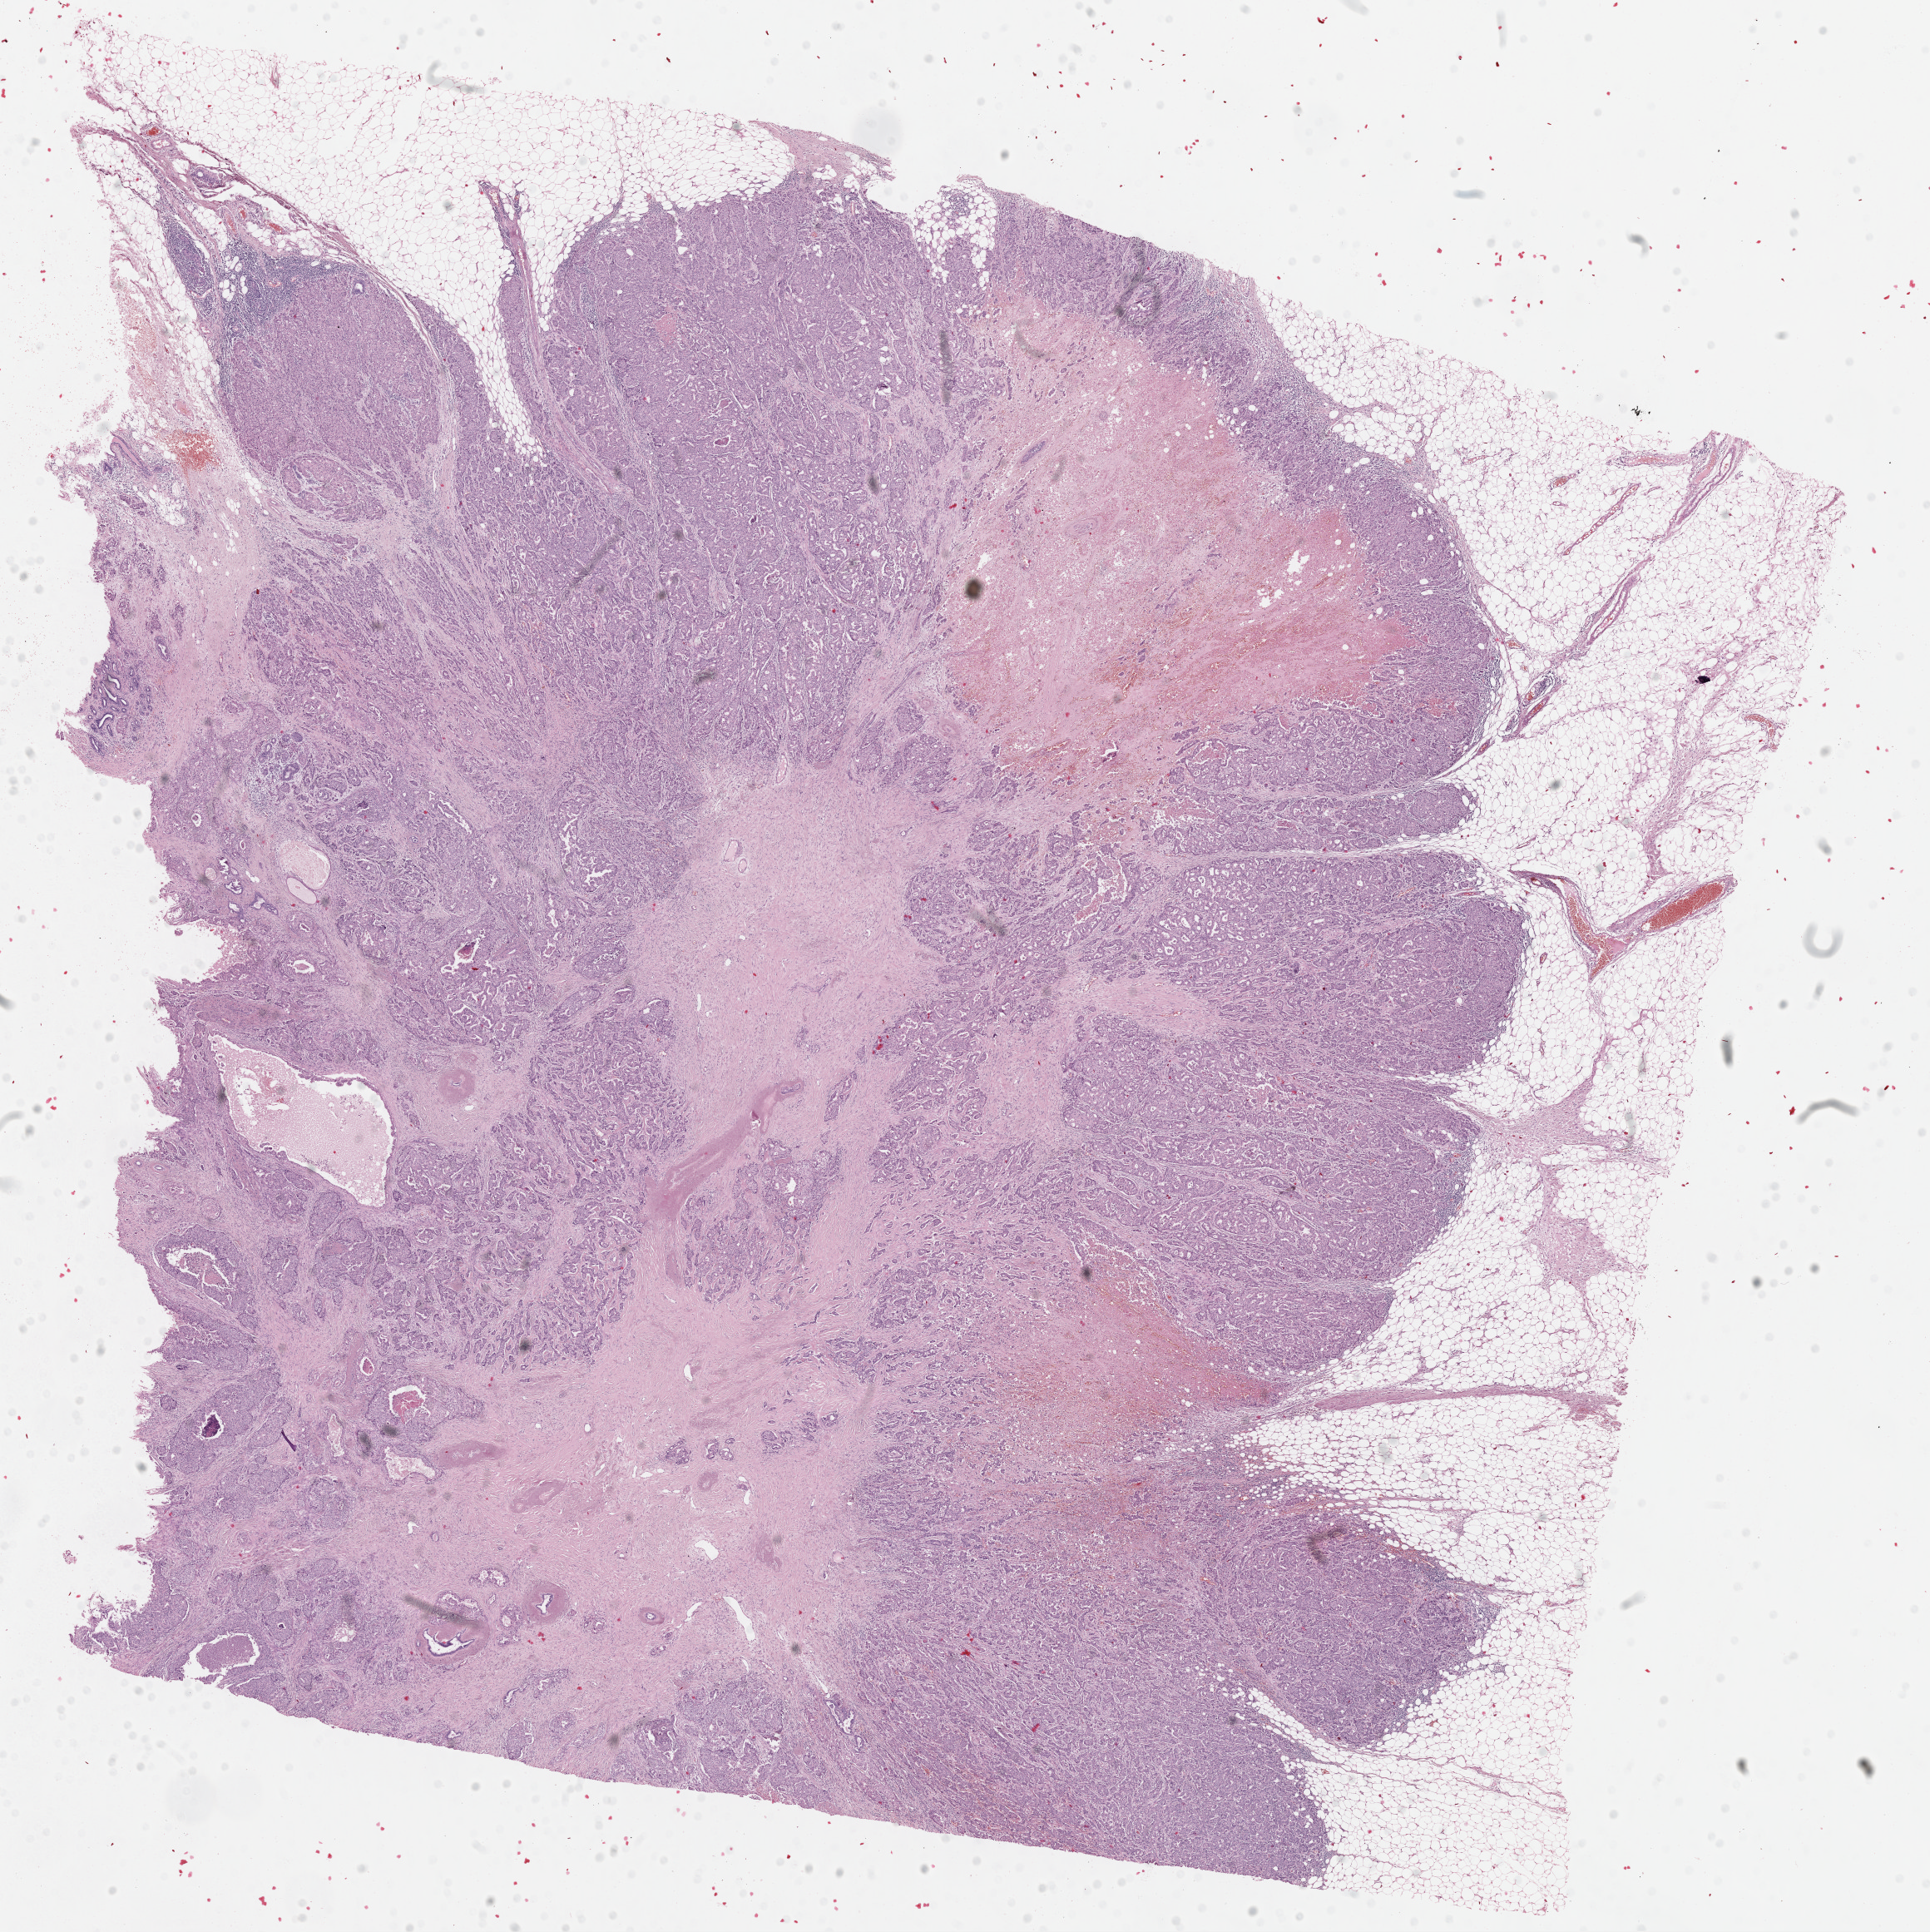
Whole-slide histology image, H&E — low-resolution overview of the scanned area, about 18.3 x 18.3 mm (slide scanned at 40x), FFPE section, primary tumour sample from the breast. Female patient; age at initial diagnosis 66 years.
Diagnosis: Infiltrating duct carcinoma, NOS.